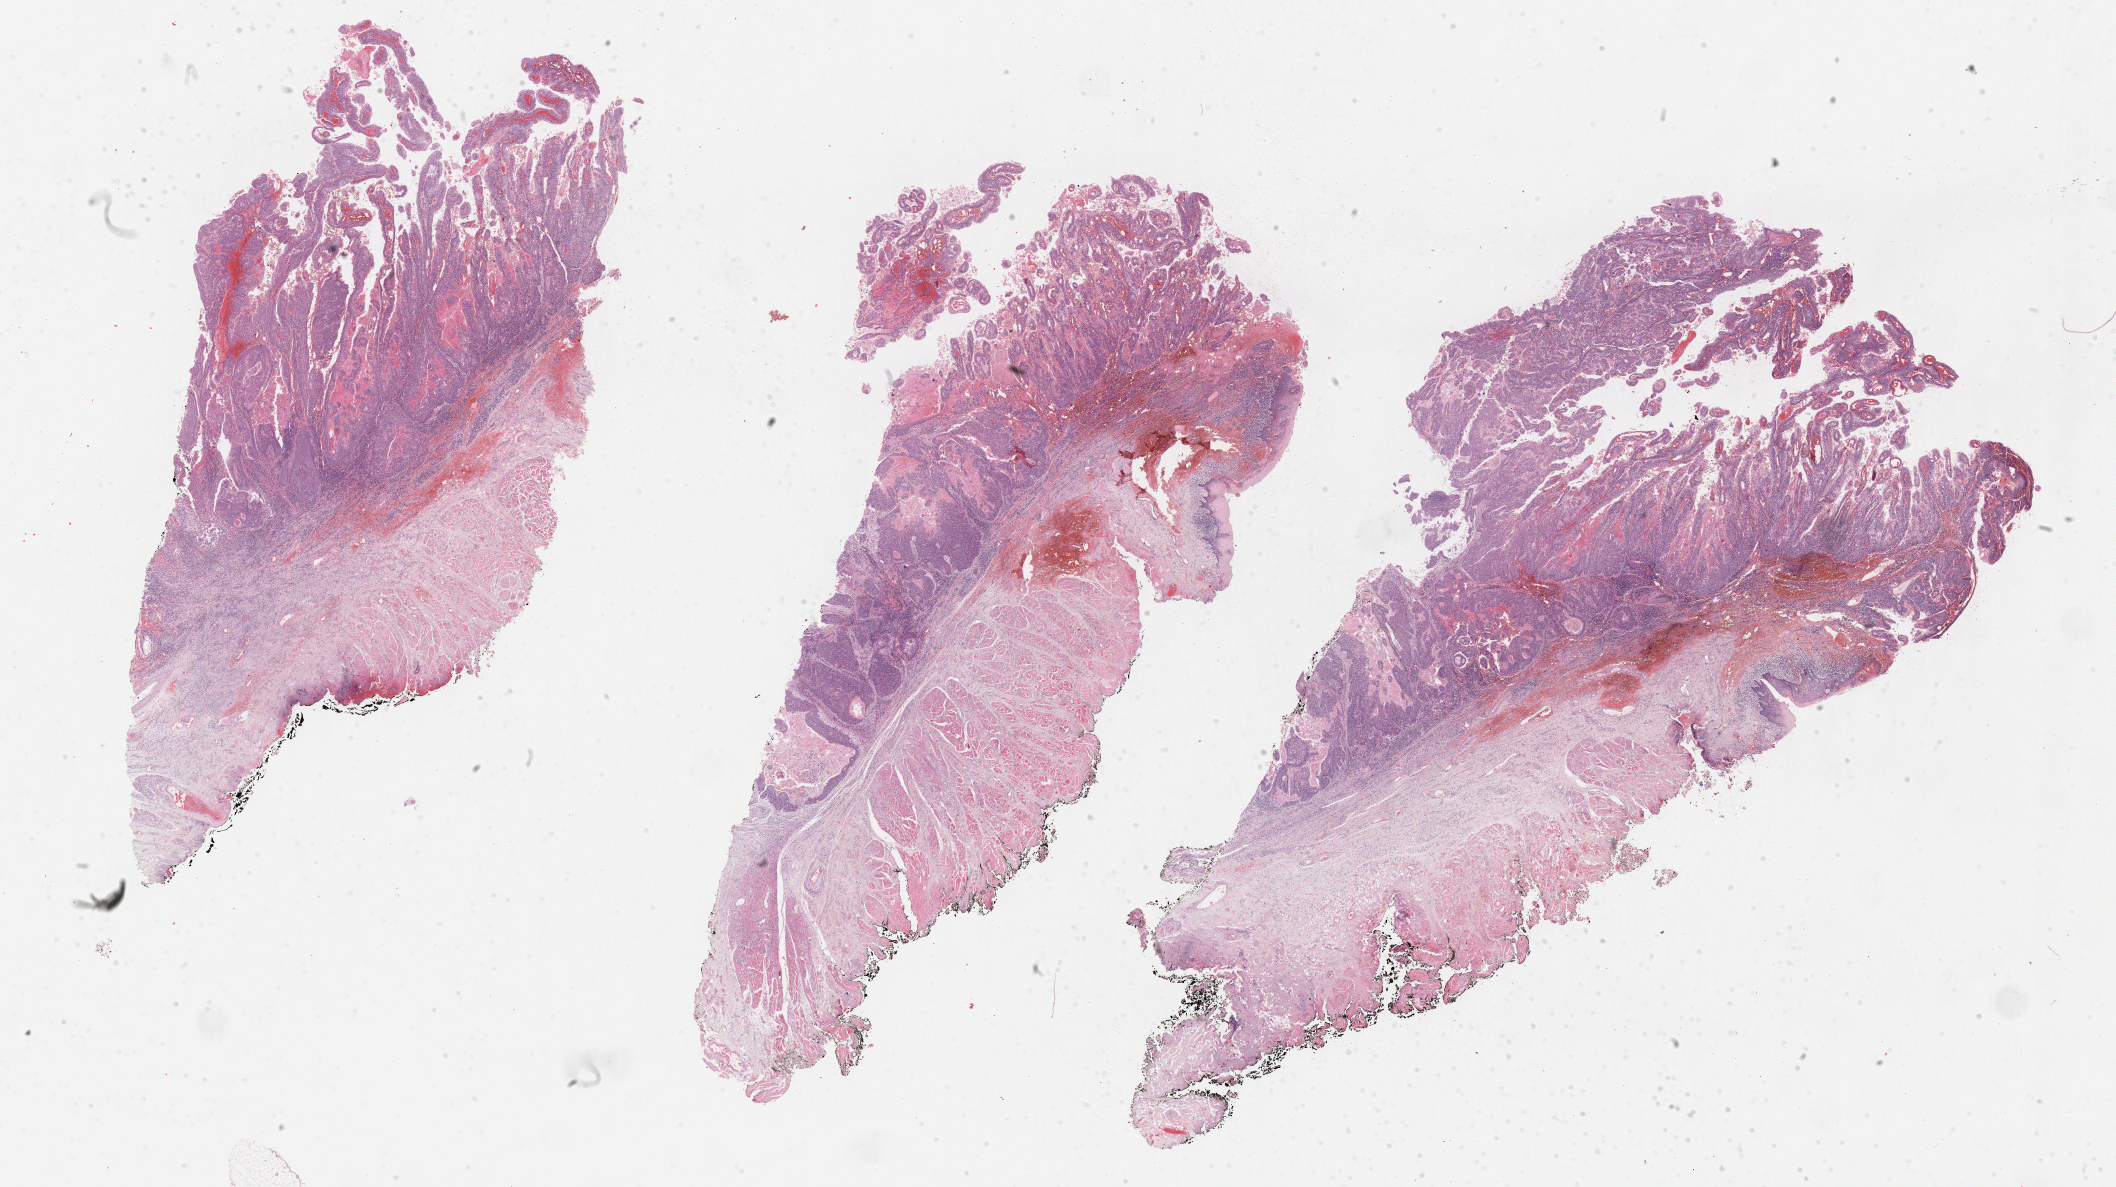
Hematoxylin and eosin (H&E) stained whole-slide image, whole scanned area (about 34.2 x 19.2 mm) shown as a low-resolution overview. FFPE section. Sample: primary tumour, head and neck. Male, age 44 years at initial diagnosis. Histologic grade: G2 (moderately differentiated).
AJCC pathologic stage: IVA. Diagnosis: Squamous cell carcinoma, keratinizing, NOS (floor of mouth, NOS).